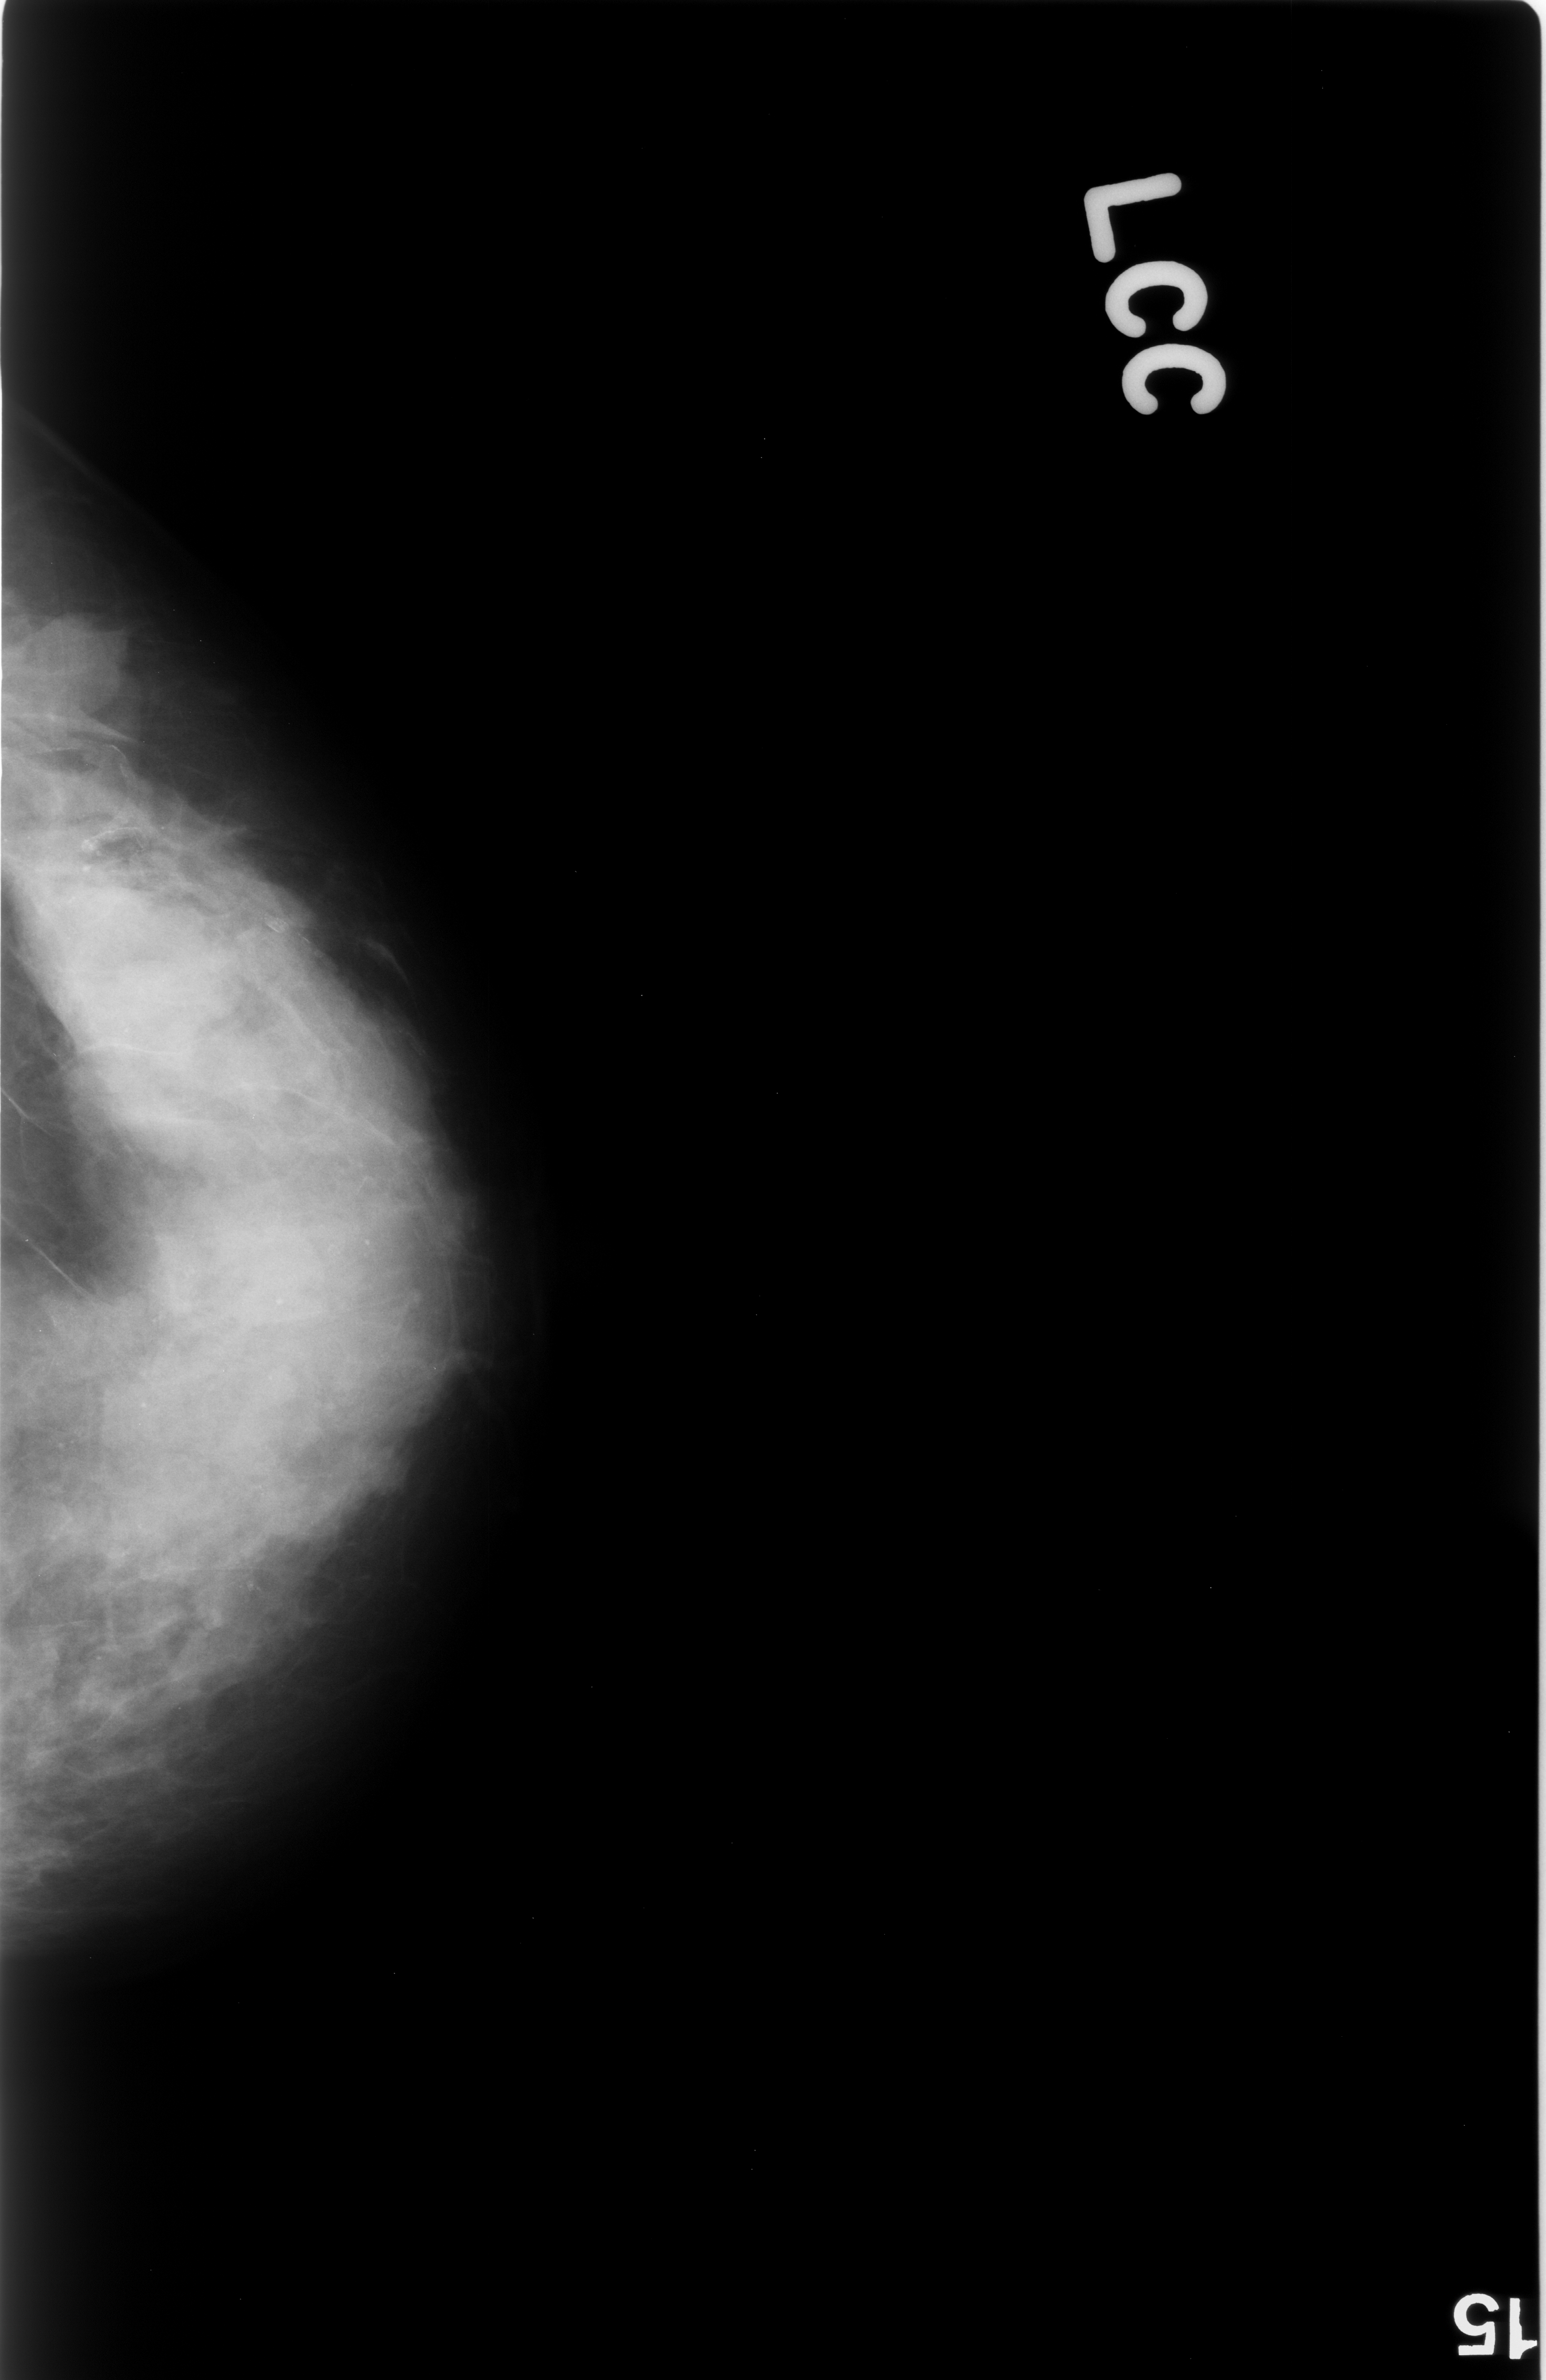
Digitized screen-film mammogram. Left breast. Craniocaudal (CC) view. Breast composition: extremely dense (BI-RADS density category 4 of 4). 1546 × 2380 image matrix.
Marked abnormalities (boxes around the expert regions of interest):
- Finding 1 of 2: mass, shape lobulated, margins circumscribed; BI-RADS assessment category 3; pathology (as recorded): benign: bounding box (x1, y1, x2, y2) in pixels: (3, 616, 134, 782)
- Finding 2 of 2: mass, shape oval, margins obscured; BI-RADS assessment category 3; subtlety rating 3 on a 1 (subtle) to 5 (obvious) scale; pathology (as recorded): benign: (62, 891, 249, 1045)